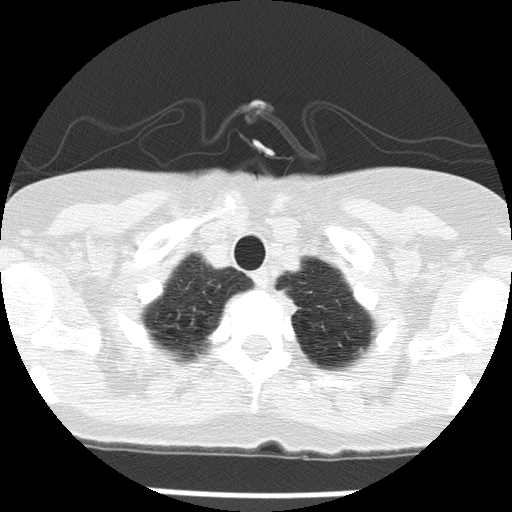
Low-dose screening chest CT, one axial slice. Position 131 of 143 along the scan axis. Reconstruction kernel FC51. 120 kVp. Lung window (W 1500 / L -600 HU). 512 × 512 image matrix, field of view 276 × 276 mm.
Annotated regions visible in this slice (outlined manually by an expert reader):
- lesion 1 (tumor, upper lobe of left lung): bounding box [x1, y1, x2, y2] px = [276, 289, 301, 315]